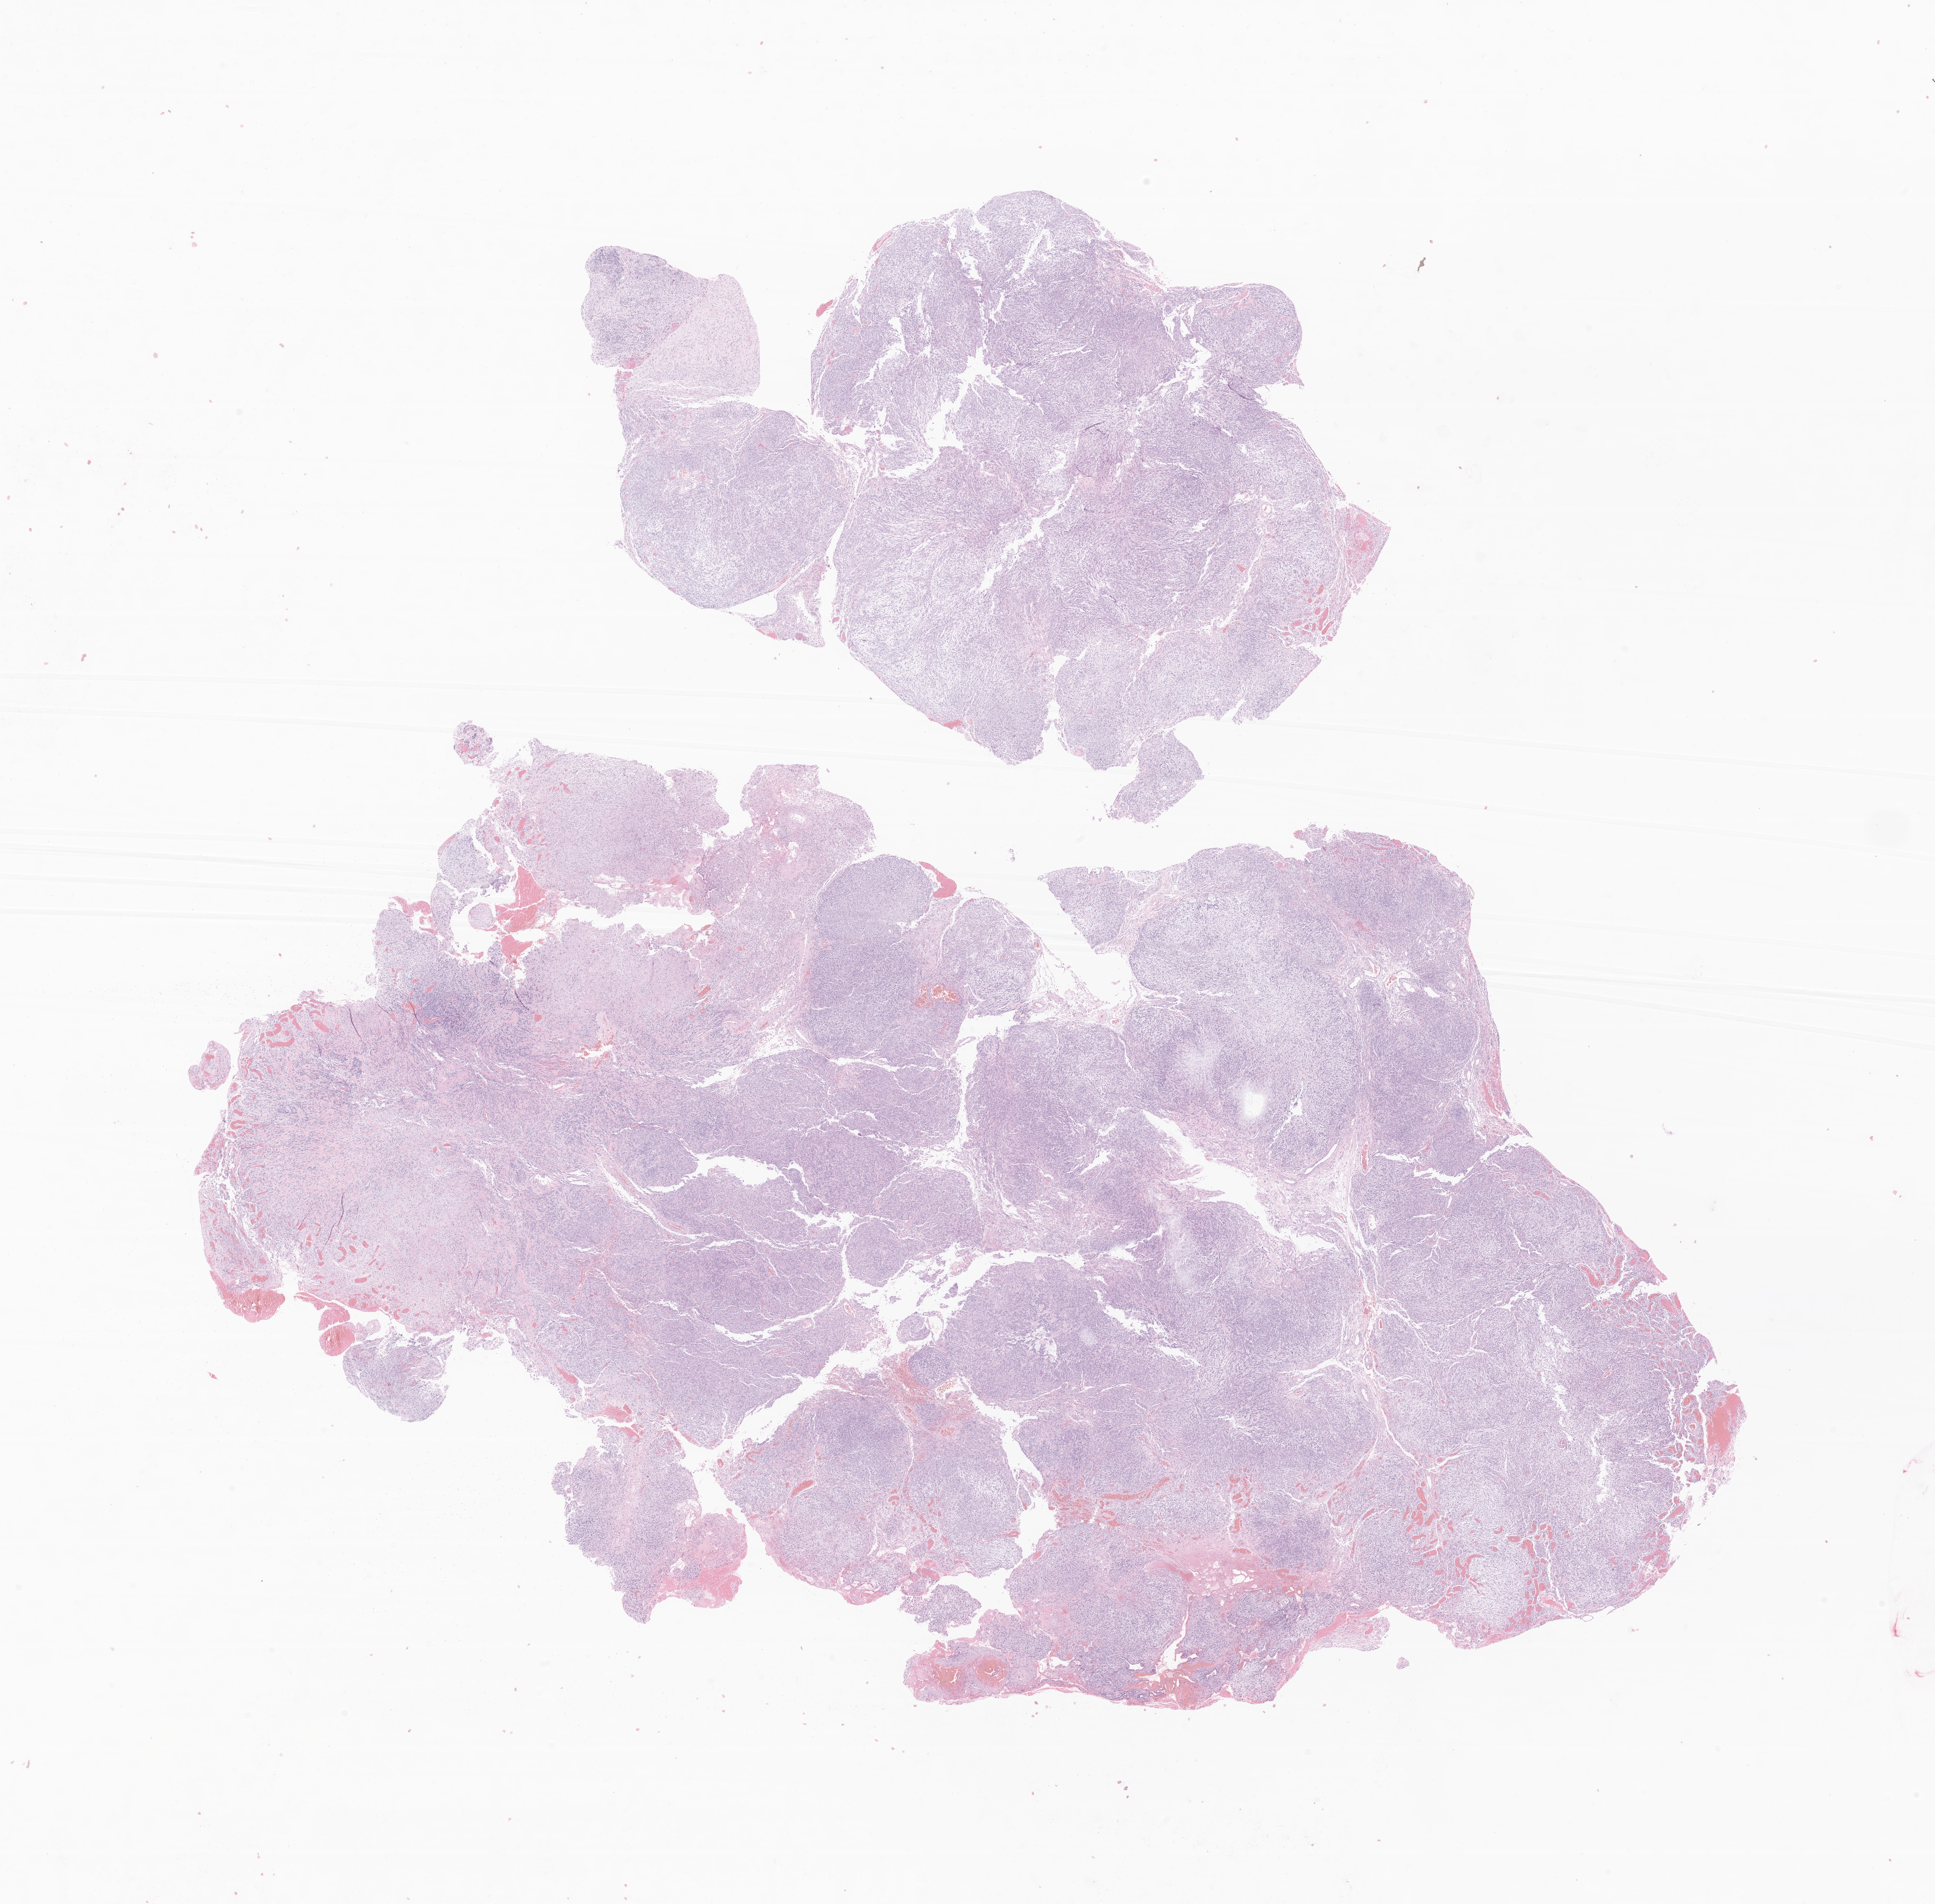
Whole-slide image, hematoxylin and eosin (H&E) stain of tumor tissue from the frontal lobe, low-resolution overview of the scanned area, about 20.0 x 19.7 mm. Formalin-fixed, paraffin-embedded (FFPE) tissue. Patient female; age 173 months (14 years 5 months).
Diagnosis: Meningioma, NOS.